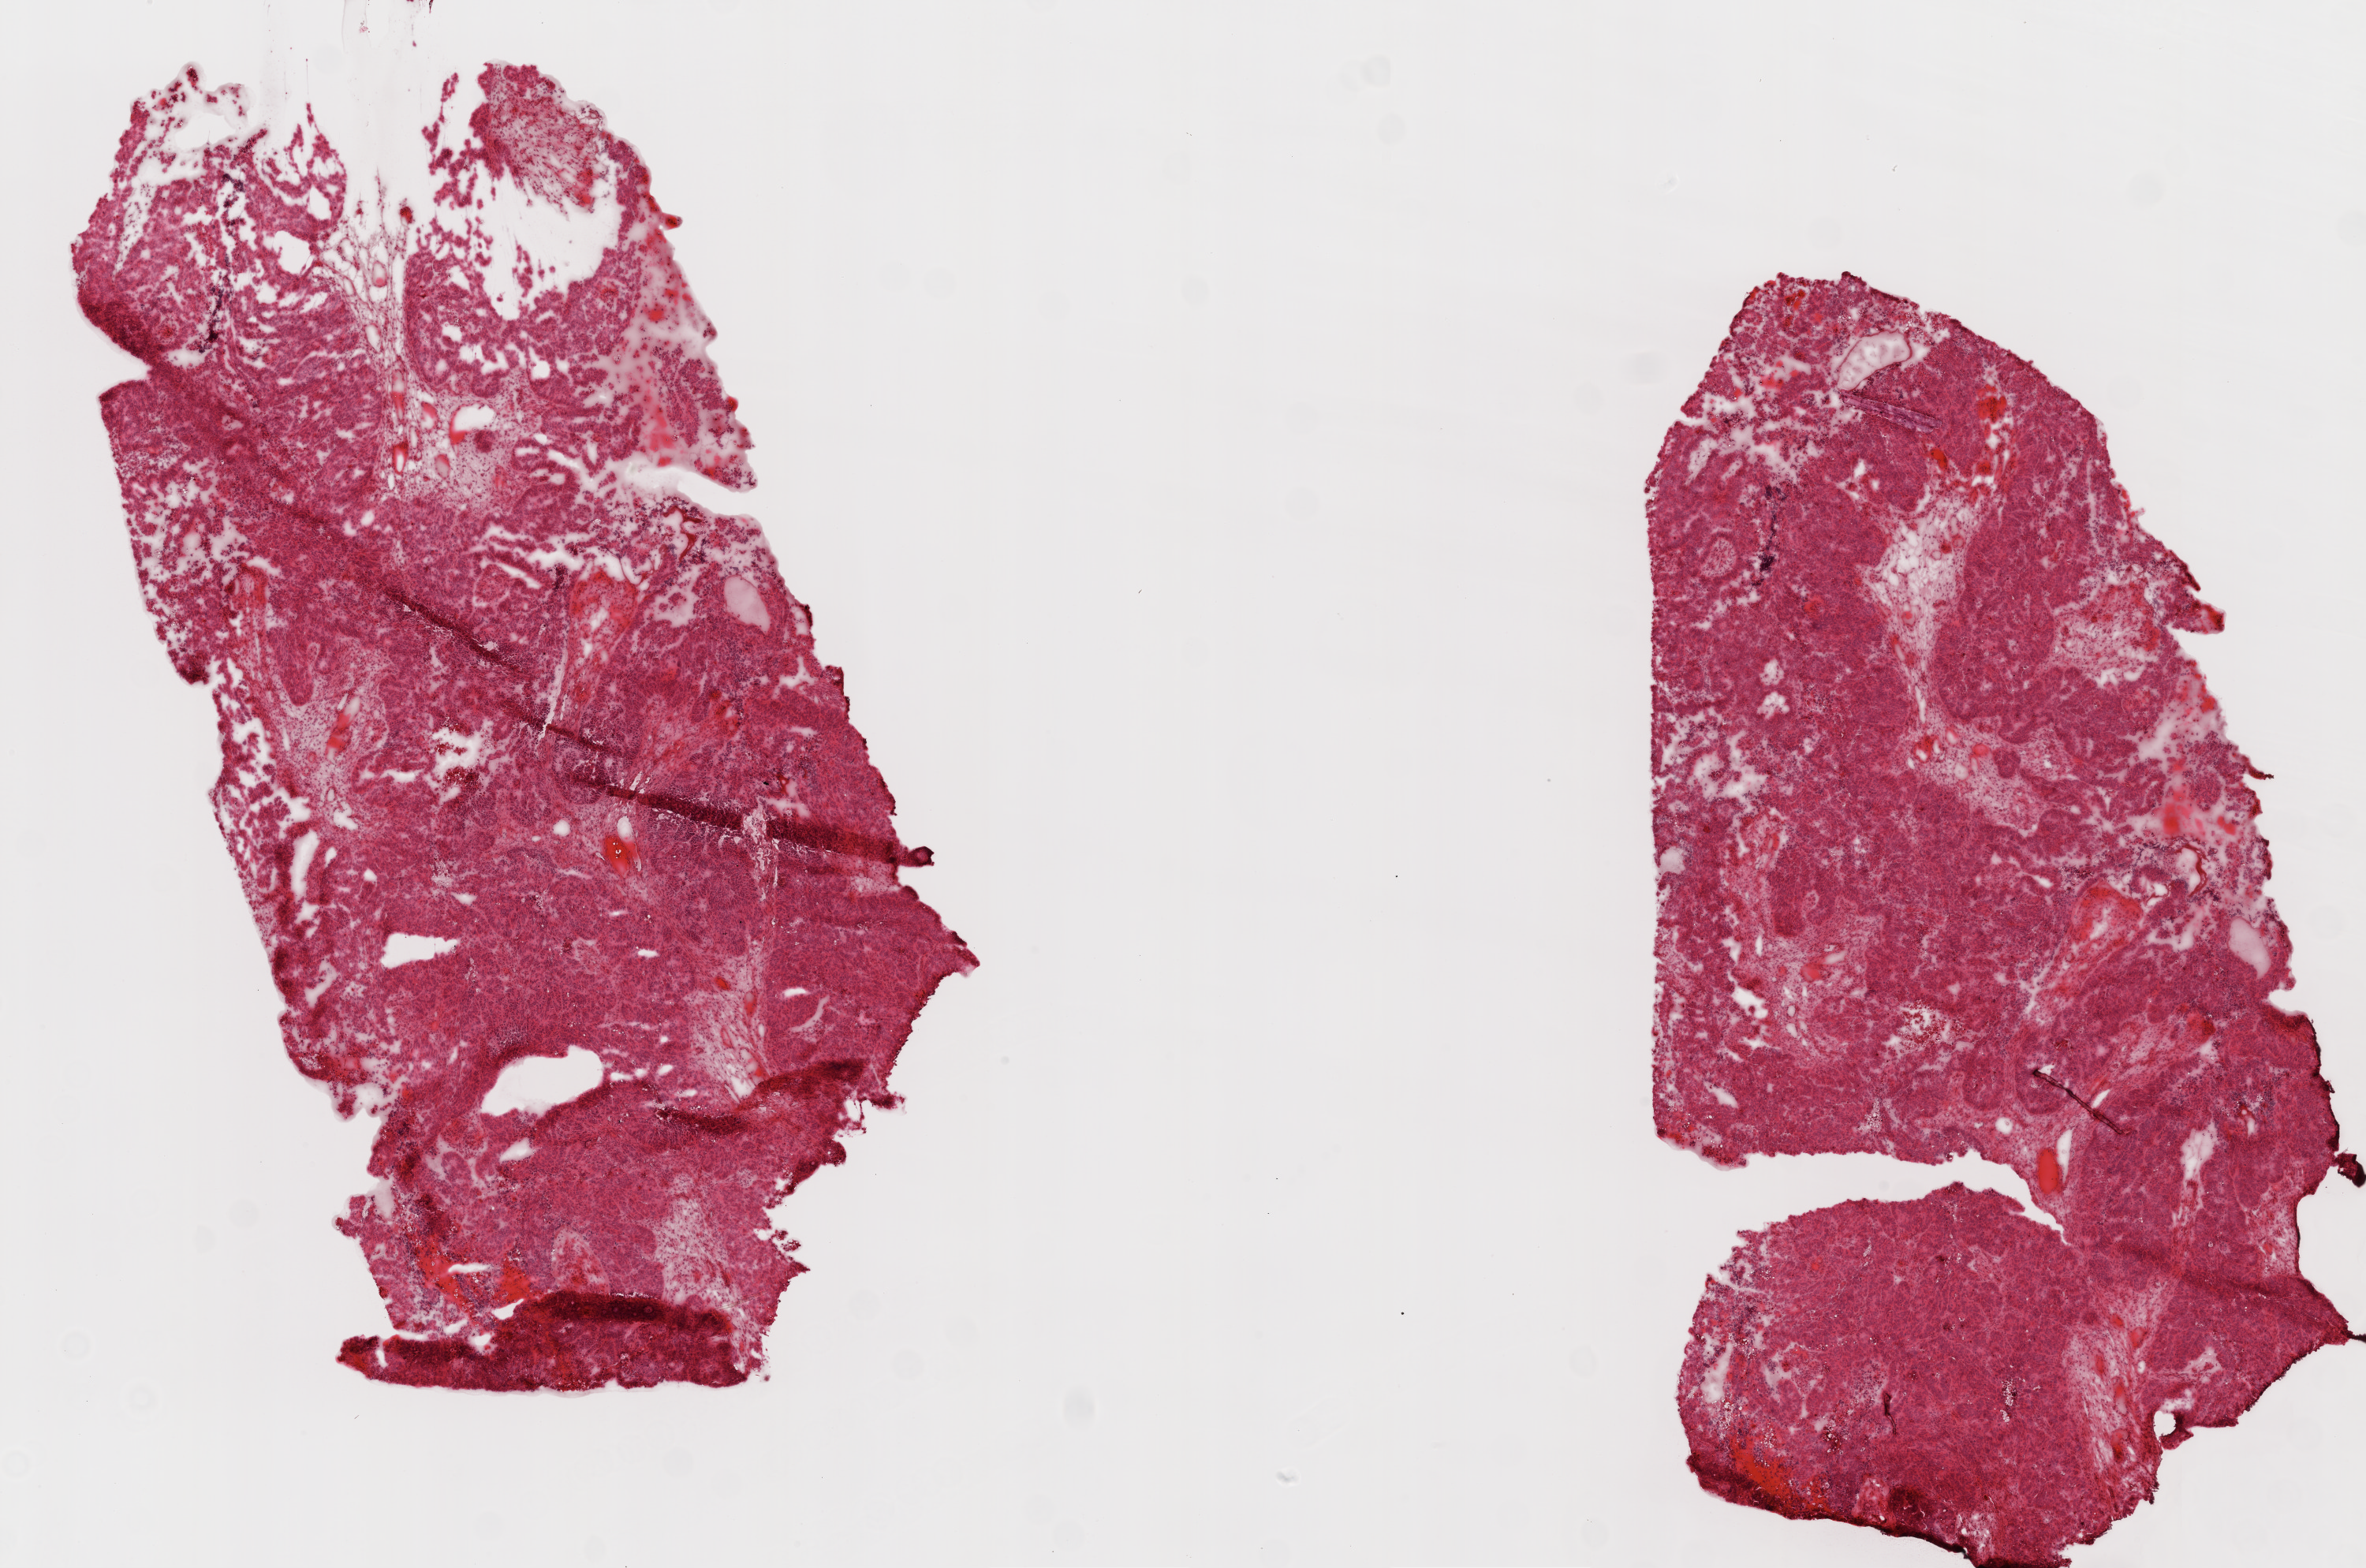
Digitized Hematoxylin and eosin (H&E) stained tissue section (whole slide), shown as a low-resolution overview of the whole scanned area (about 12.0 x 8.0 mm), frozen section from the top of the tissue portion, sample: primary tumour, ovary. Female patient; age at initial diagnosis 67 years. Slide review estimates, as recorded: tumour cells 65%, tumour nuclei 95%.
Pathologic diagnosis: Serous cystadenocarcinoma, NOS.